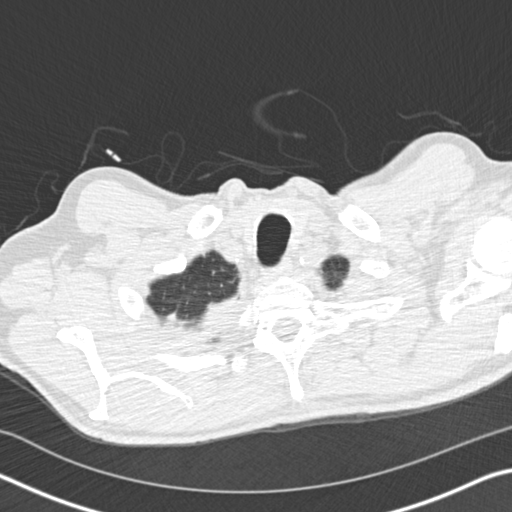
Low-dose screening chest CT, one axial slice; position 162 of 175 along the scan axis; reconstruction kernel B30f; 120 kVp; lung window (W 1500 / L -600 HU); 2 mm slice thickness; 512 × 512 image matrix, field of view 340 × 340 mm.
Outlined on this slice (outlined manually by an expert reader):
- lesion 1 (tumor, upper lobe of right lung): bounding box <203,294,239,332> (left, top, right, bottom; pixels)